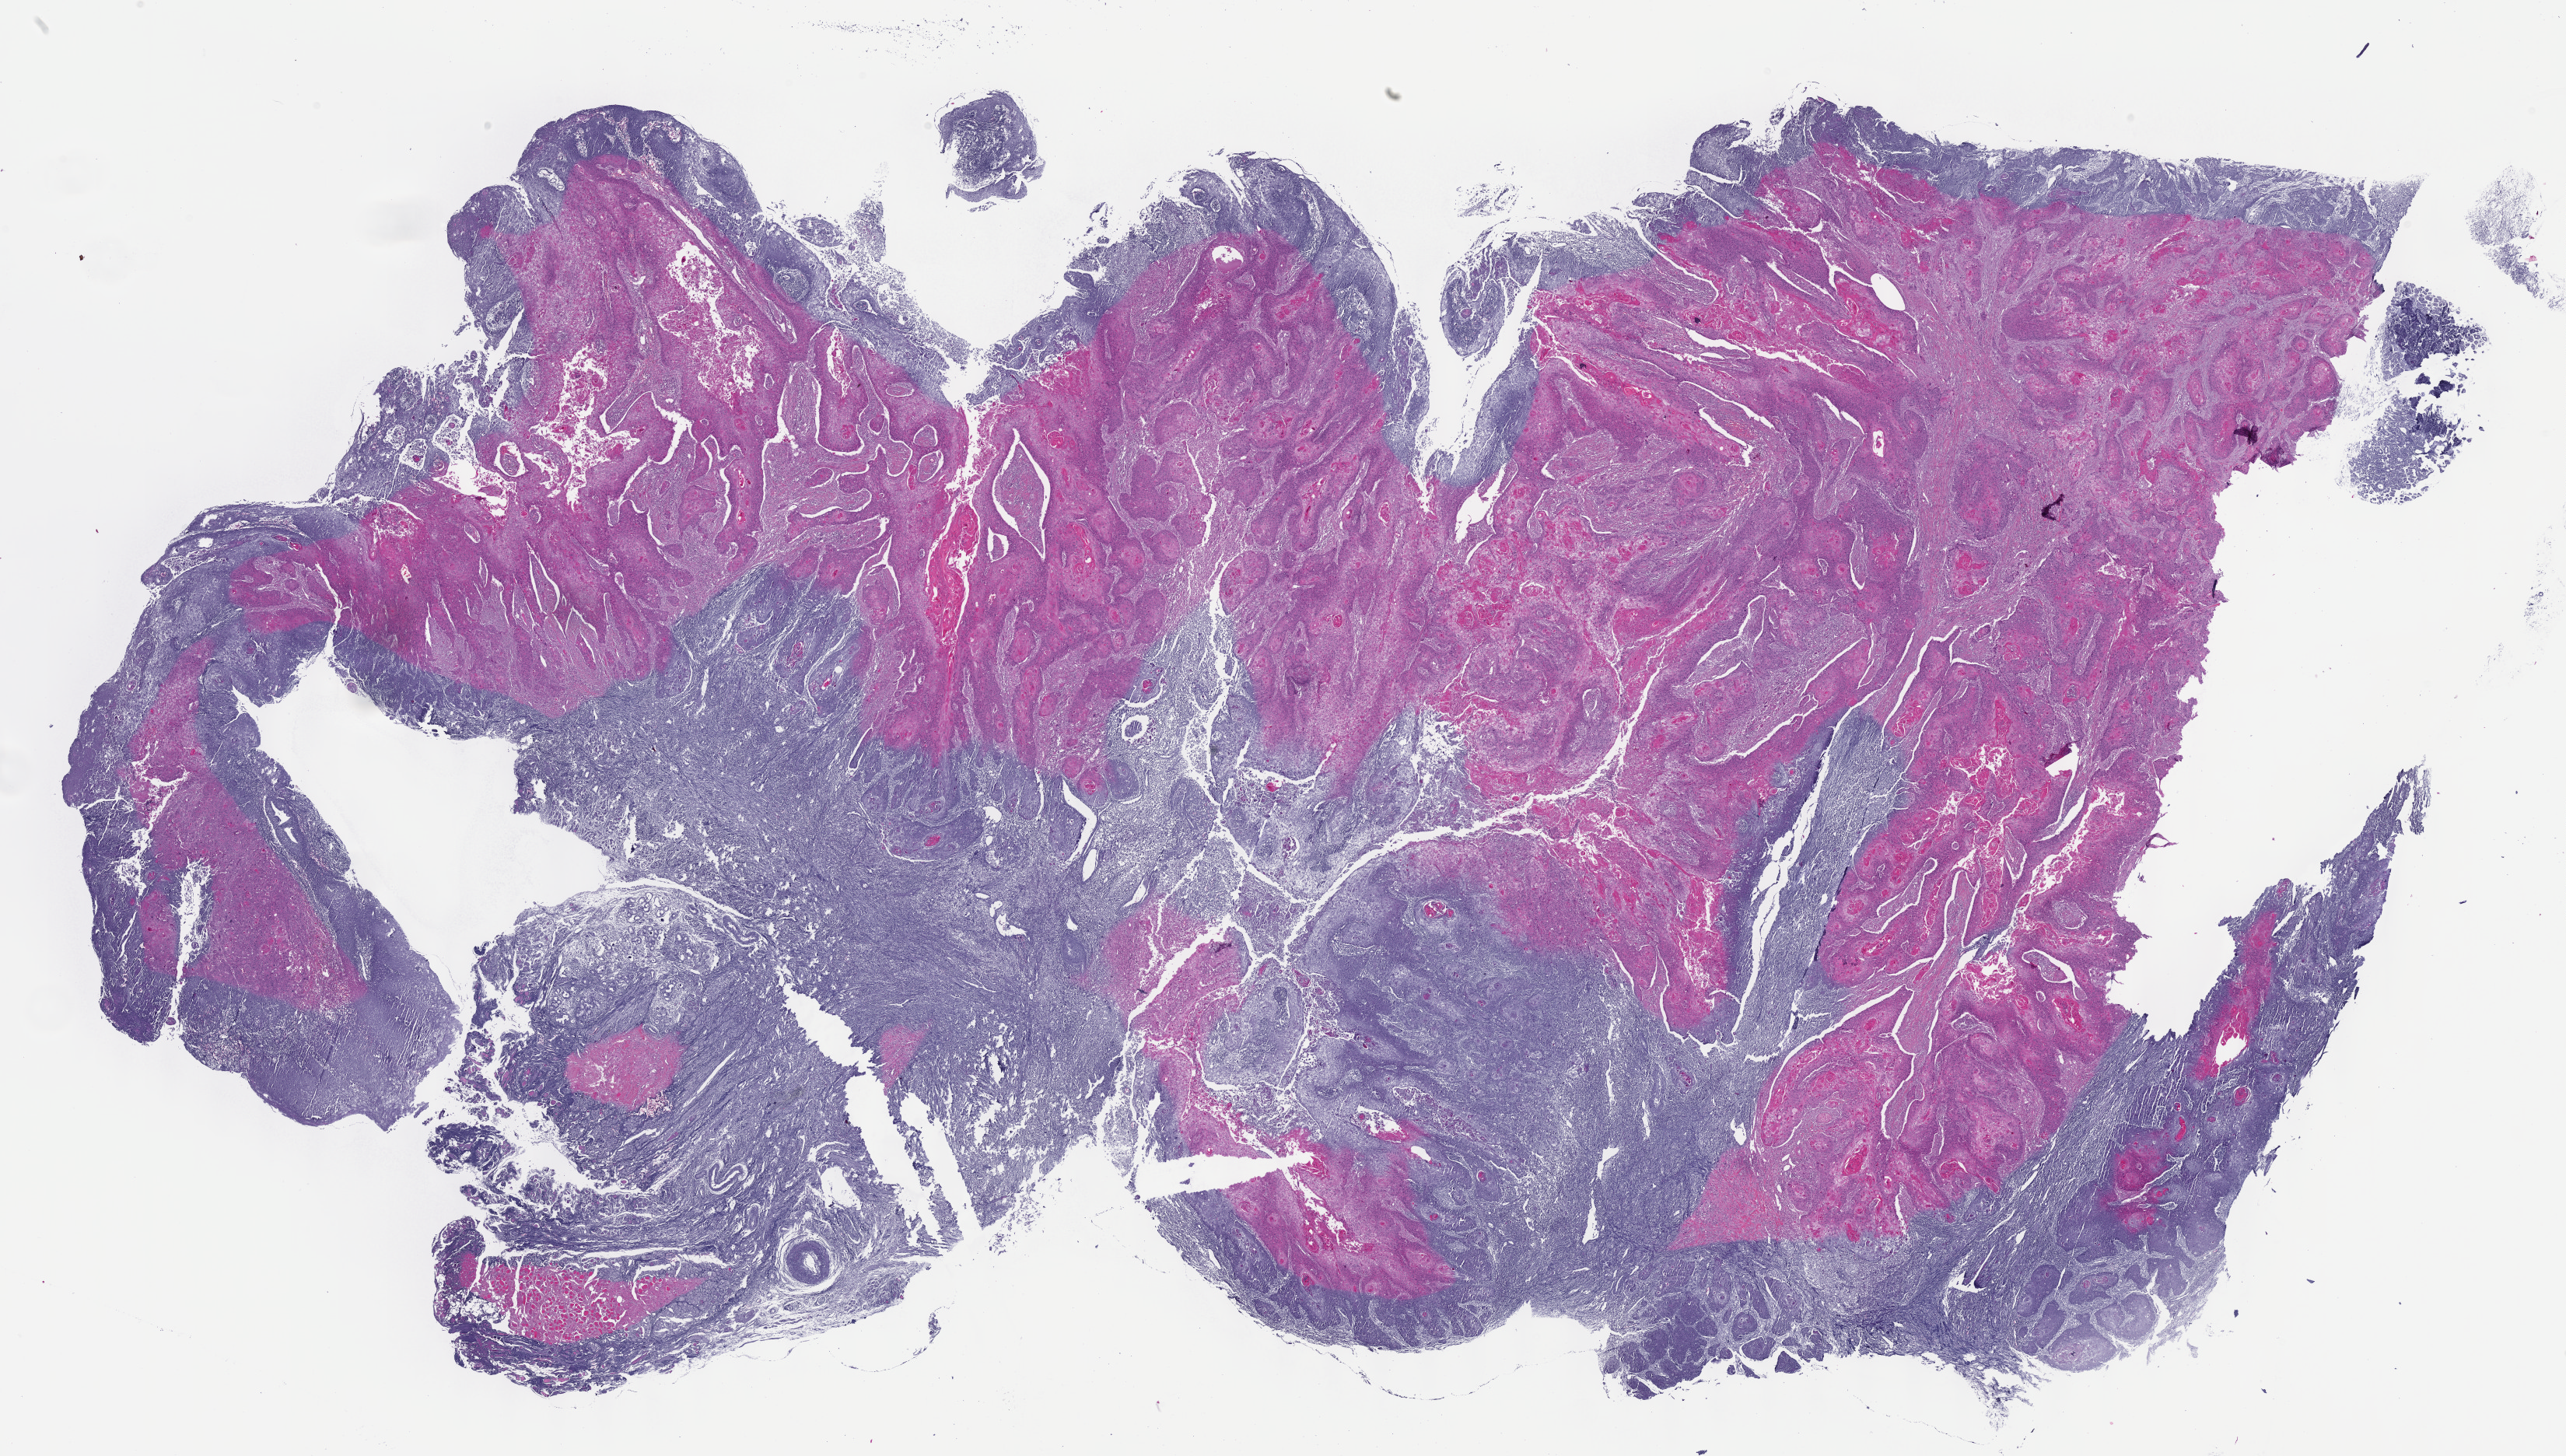
Digitized Hematoxylin and eosin (H&E) stained tissue section (whole slide), shown as a low-resolution overview of the whole scanned area (about 26.7 x 15.1 mm); formalin-fixed paraffin-embedded (FFPE) diagnostic section; sample: primary tumour, head and neck. Male, age 79 years at initial diagnosis. Histologic grade: G1 (well differentiated).
- AJCC pathologic stage: II (7th edition)
- diagnosis: Squamous cell carcinoma, NOS (overlapping lesion of lip, oral cavity and pharynx)